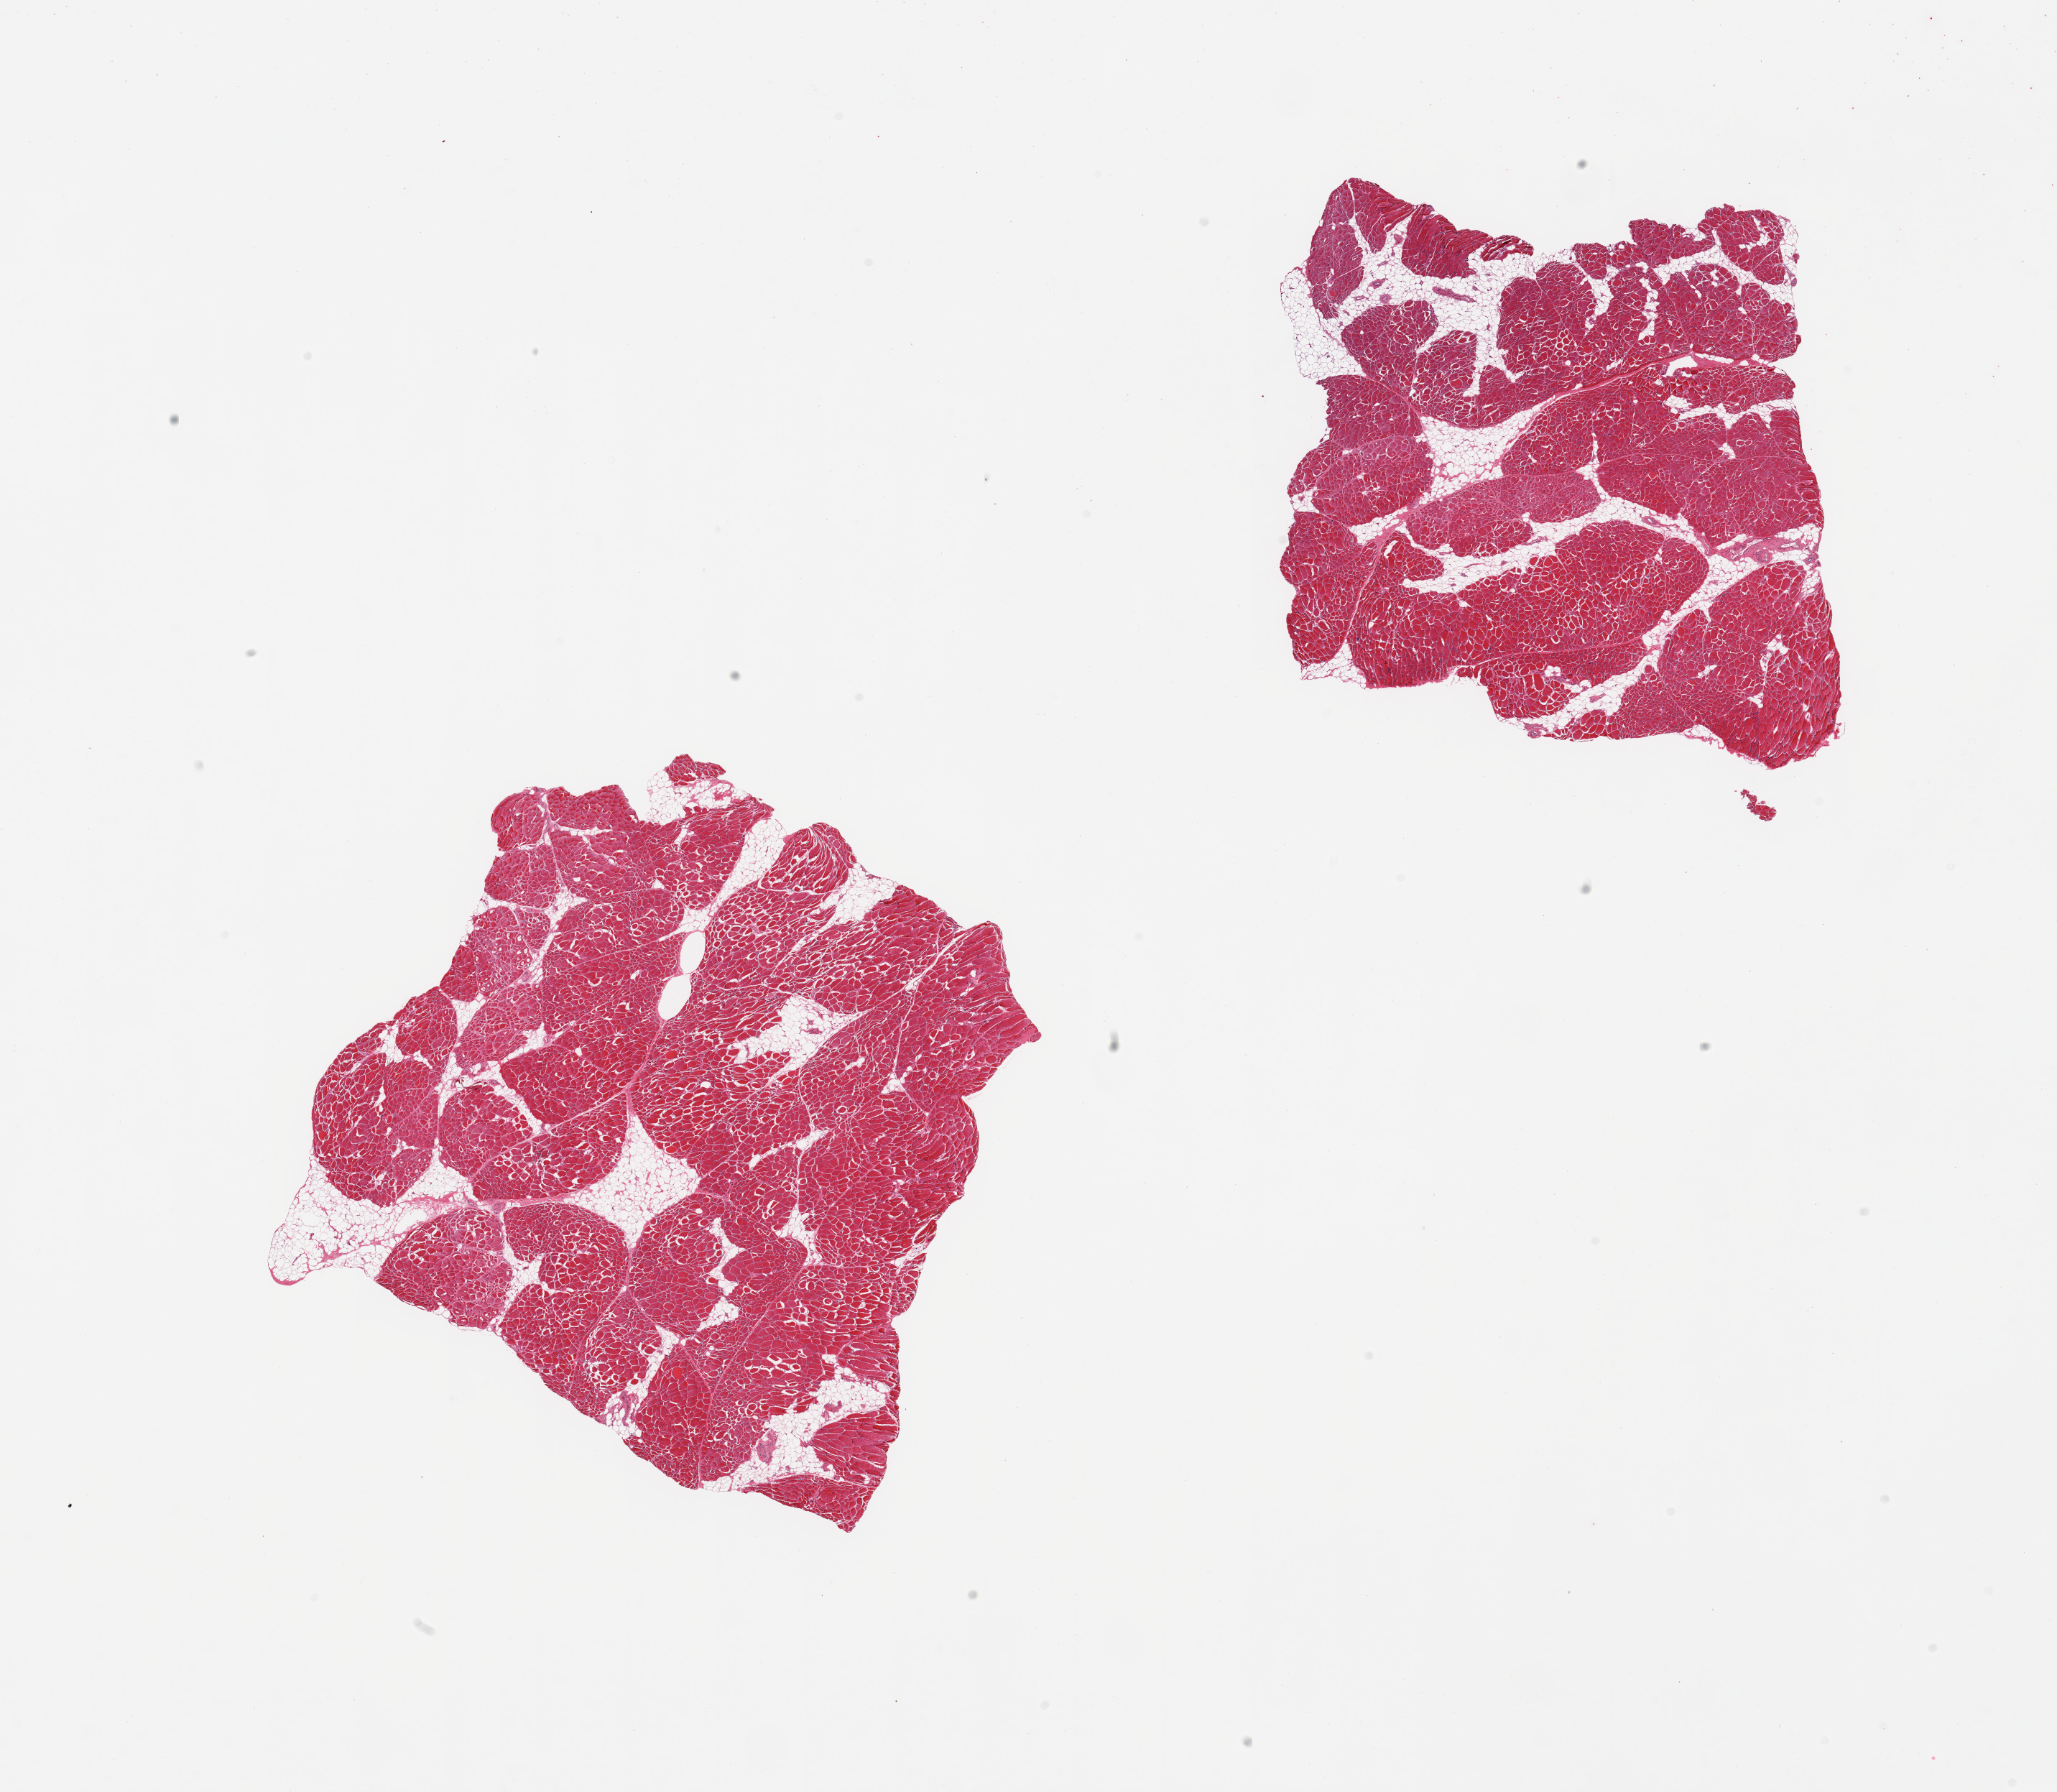
H&E whole-slide image, a low-resolution overview of the entire scanned area, about 22.6 x 19.7 mm; PAXgene-fixed paraffin-embedded (PFPE) section; sampled site (target tissue): skeletal muscle; tissue donor sample. Female donor.
Pathologist's review note for this sample: 2 pieces, ~20% interstitial fat/vessel.